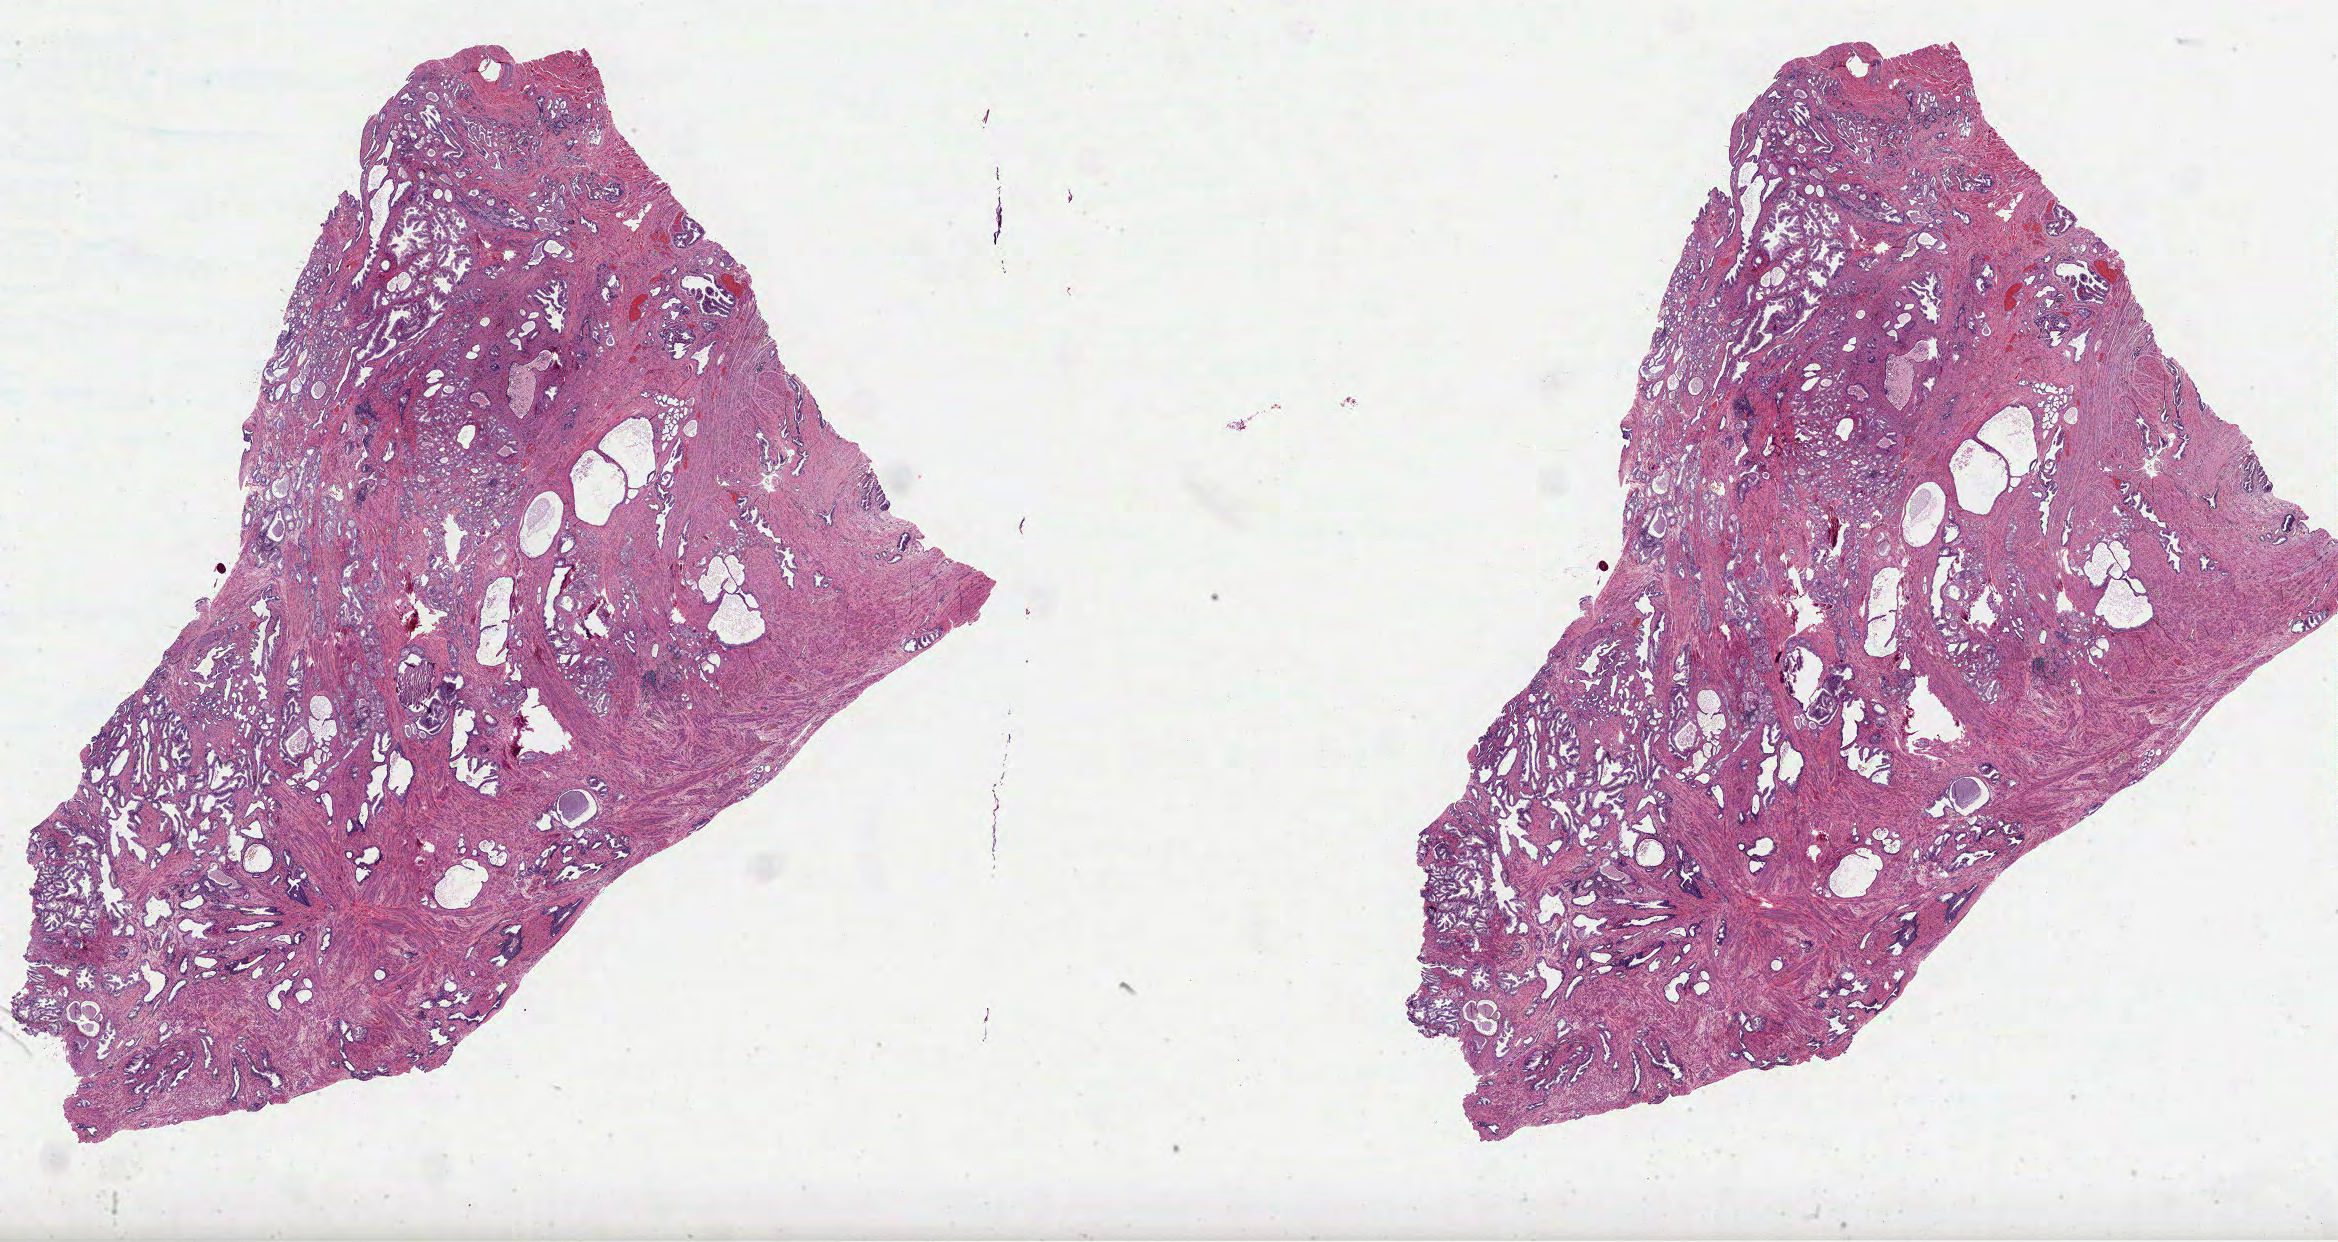
H&E whole-slide image, low-resolution overview of the scanned area, about 37.7 x 20.0 mm (slide scanned at 40x), formalin-fixed paraffin-embedded (FFPE) diagnostic section, prostate, primary tumour sample. Male patient; age at initial diagnosis 61 years. Gleason score: 7 (3+4).
Lymph nodes positive (case pathology): 0 of 17 examined. Diagnosis: Acinar cell carcinoma (prostate gland).